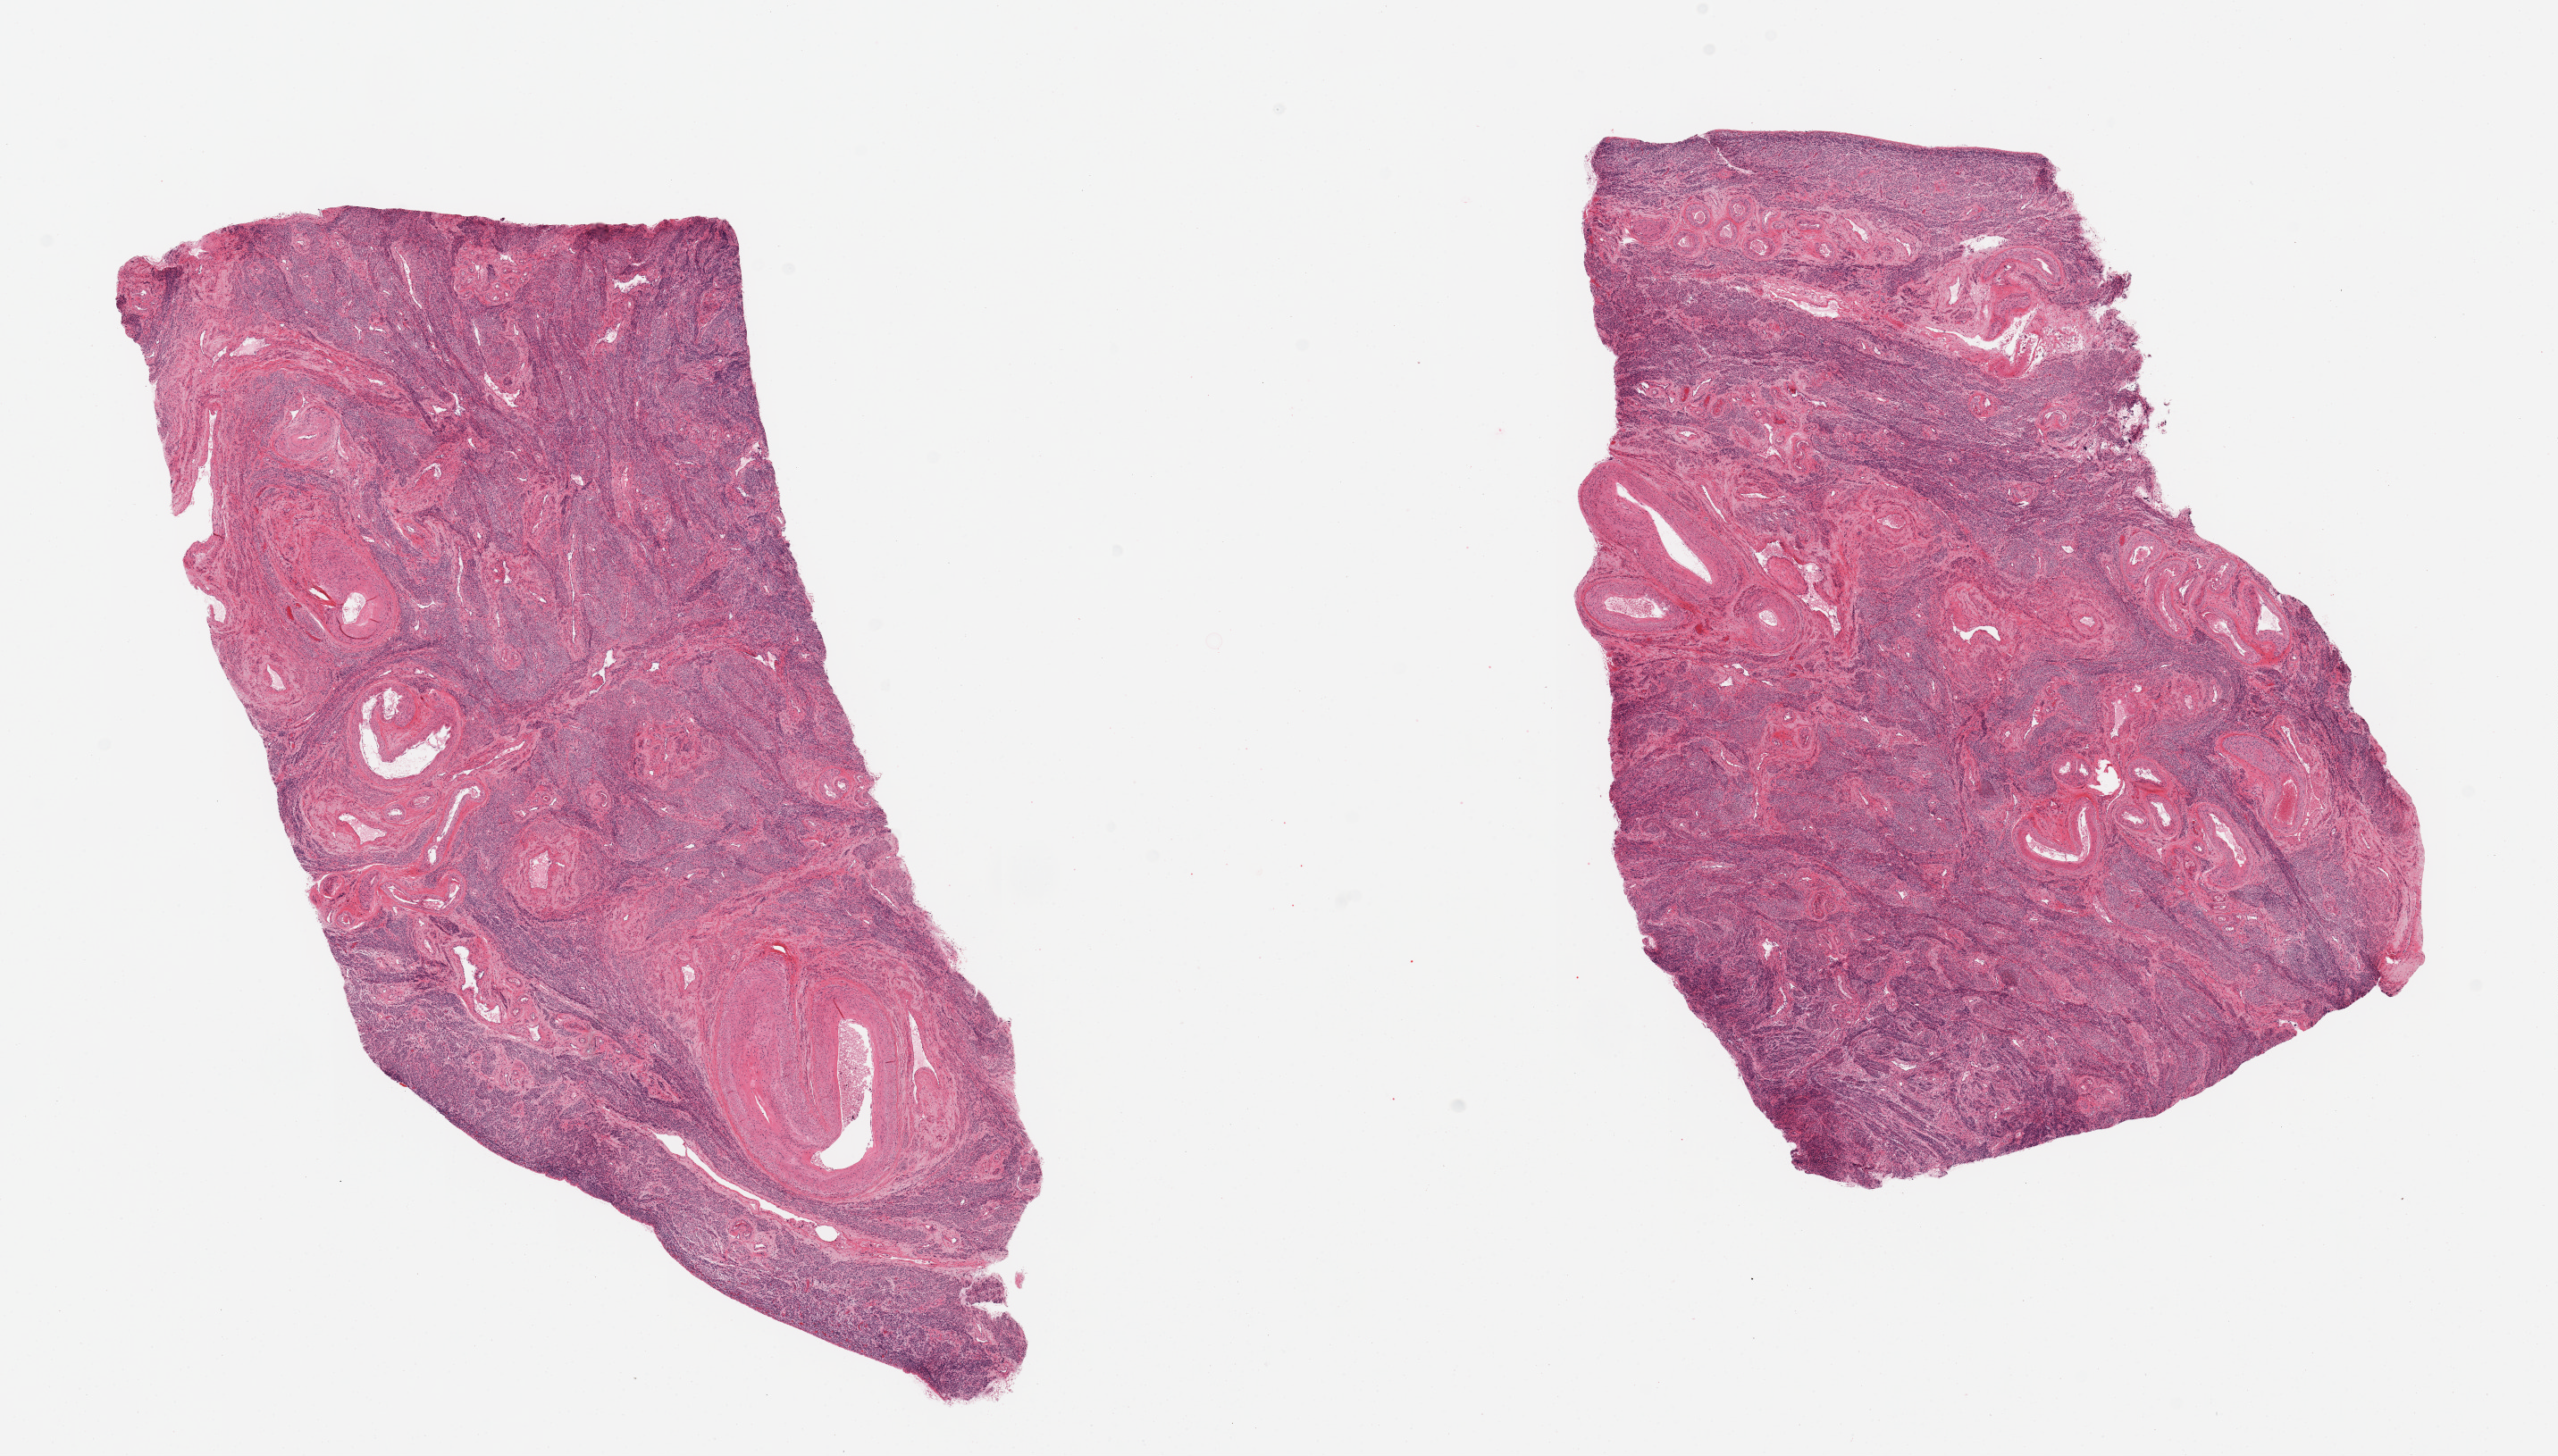
Haematoxylin and eosin whole-slide image, shown as a low-resolution overview of the whole scanned area (about 22.6 x 12.9 mm), PAXgene-fixed, paraffin-embedded tissue, target tissue: uterus, donor tissue sample. Donor: female.
- review note (as recorded): 2 pieces; myometrium only